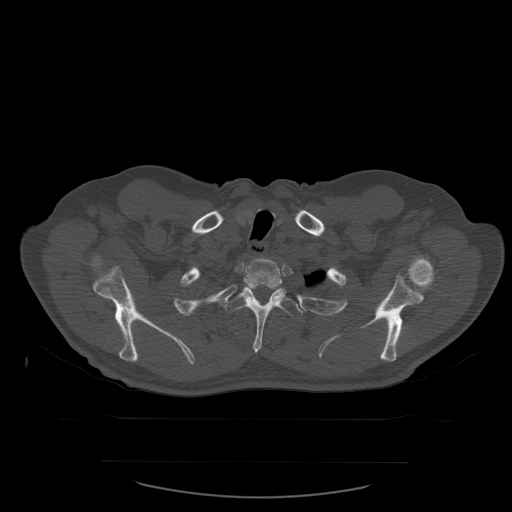
CT including the spine, one axial slice. Position 466 of 590 along the scan axis. Bone window (W 1800 / L 400 HU). 1.25 mm slice thickness. 512 × 512 image matrix, field of view 479 × 479 mm. Patient age 71 years. From the clinical record (not read from this slice): primary cancer: lung; vertebrae with lytic lesions (as recorded): T1, T2, L5, S1.
Outlined on this slice (semi-automatic segmentation, software-assisted and operator-edited):
- T2 vertebra: bounding box [x1, y1, x2, y2] px = [244, 258, 283, 290]
- T3 vertebra: [224, 288, 304, 354]